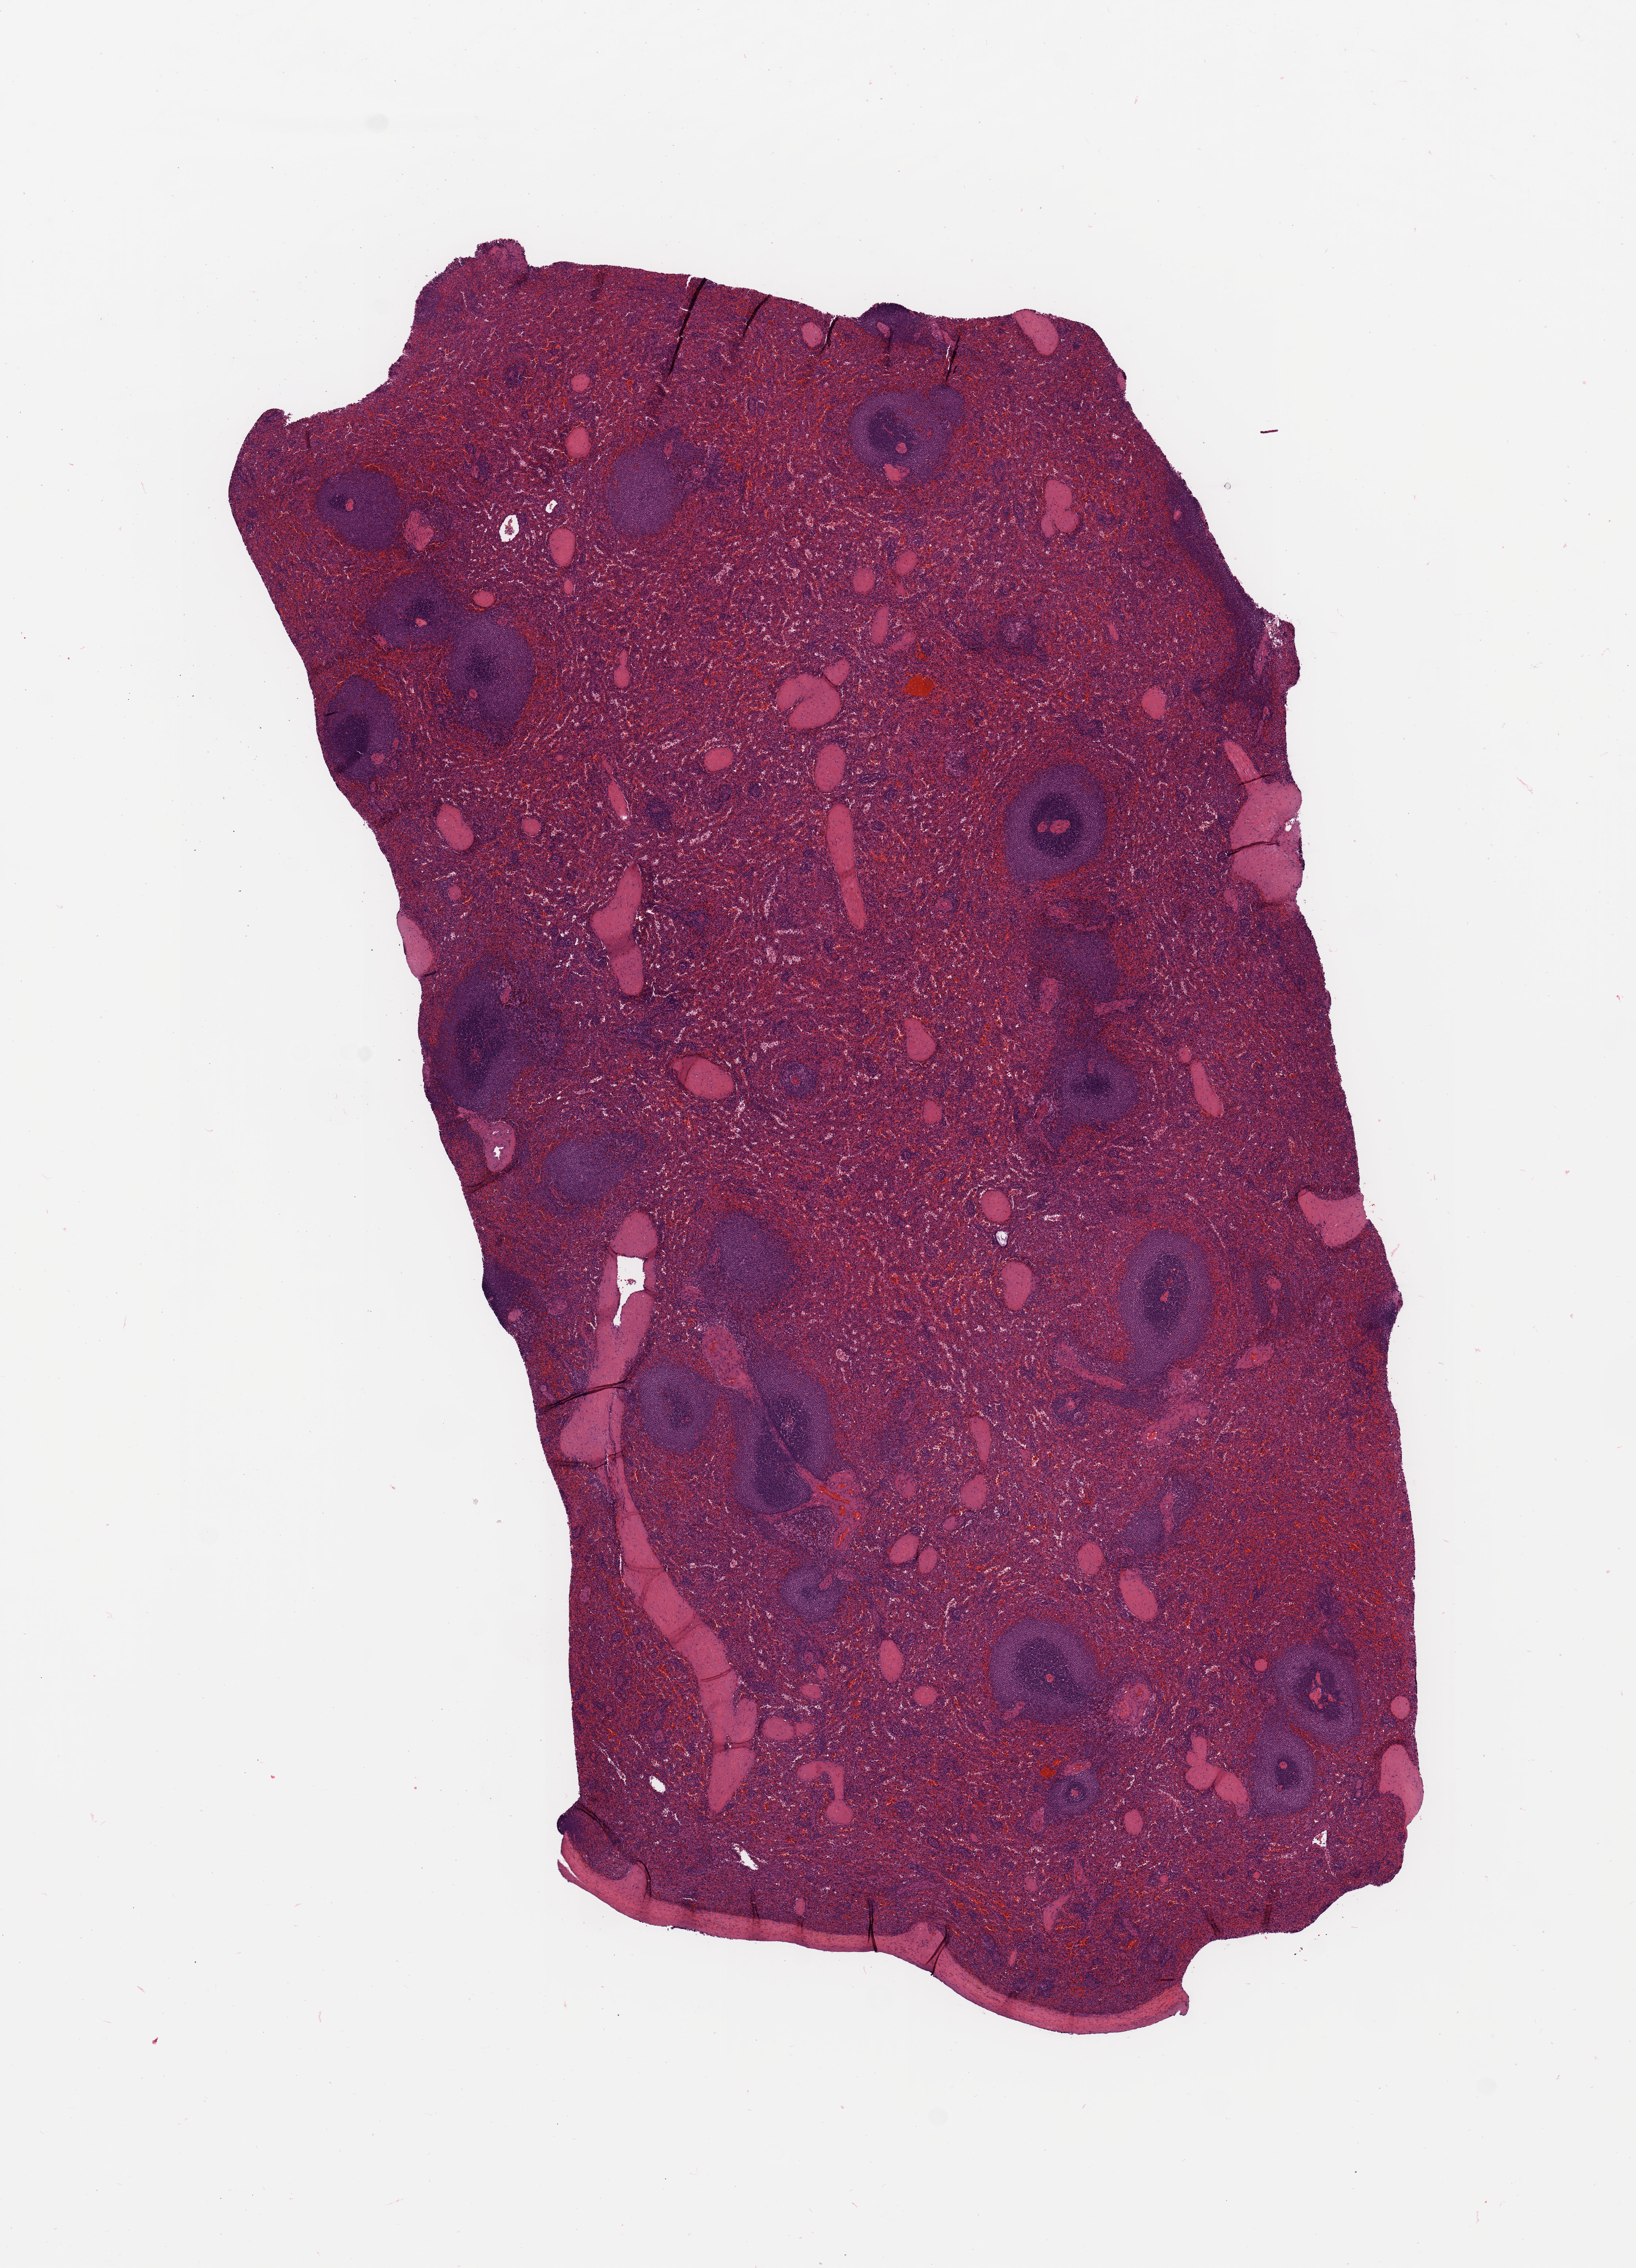
Whole-slide histology image, H&E-stained — low-resolution overview of the scanned area, about 8.9 x 12.3 mm (acquisition: 20x scan), normal (non-tumour) tissue sample, sampled site: pancreas. 69-year-old male patient.
This section: normal (non-tumour) tissue from the same patient. Patient diagnosis: Infiltrating duct carcinoma, NOS.